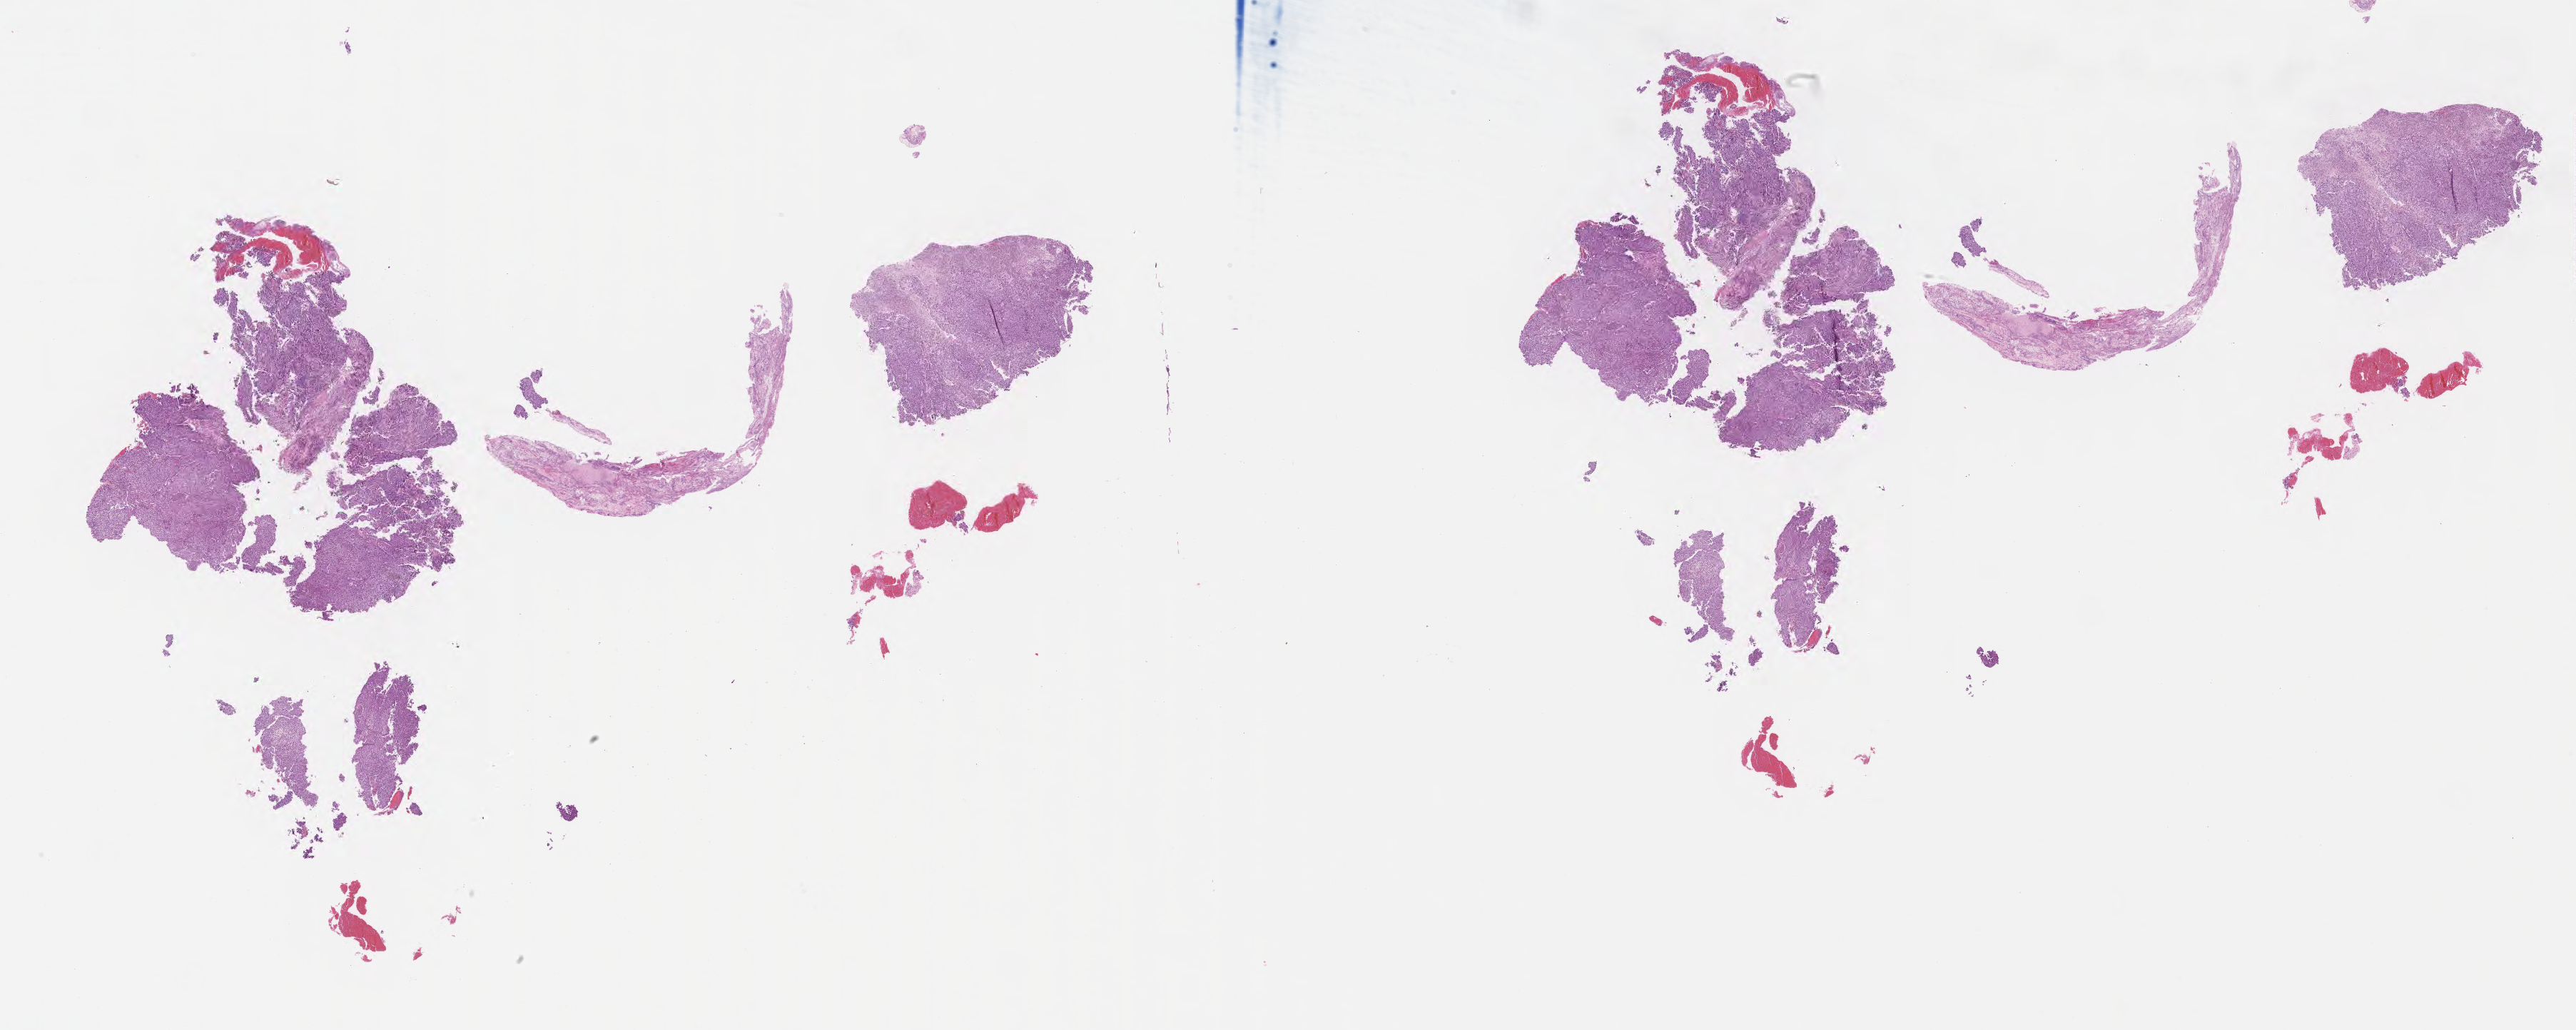
Whole-slide image, haematoxylin and eosin stain, a low-resolution overview of the entire scanned area, about 29.2 x 11.7 mm. Tumor tissue. Anatomic site: cervix. Female patient, aged 33.
• histologic diagnosis: Squamous cell carcinoma, large cell, nonkeratinizing, NOS